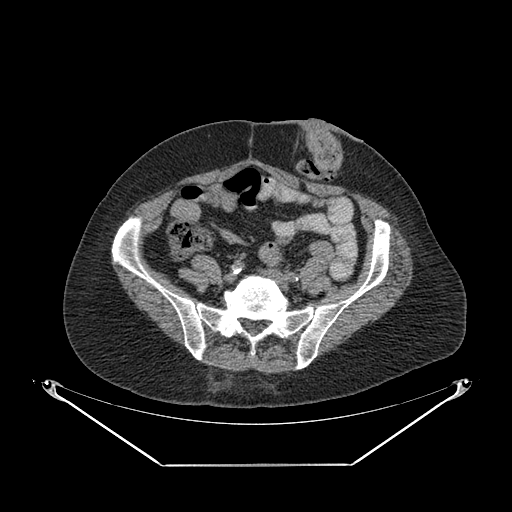
CT of an extremity soft-tissue mass (from a PET/CT study), one axial slice; slice 81 of 267 in the series (ordered by position); reconstruction kernel SOFT; soft-tissue window (W 400 / L 40 HU); 3.75 mm slice thickness; 512 × 512 image matrix, field of view 500 × 500 mm. Female patient. From the clinical record (not read from this slice): histological type: spindle cell suggestive of myxofibrosarcoma; grade: intermediate; site of the primary tumour: right buttock.
Annotated regions visible in this slice (expert contour drawn on MRI and transferred to this co-registered scan by the dataset authors):
- gross tumour volume (mass): bounding box <185,351,239,382> (left, top, right, bottom; pixels)